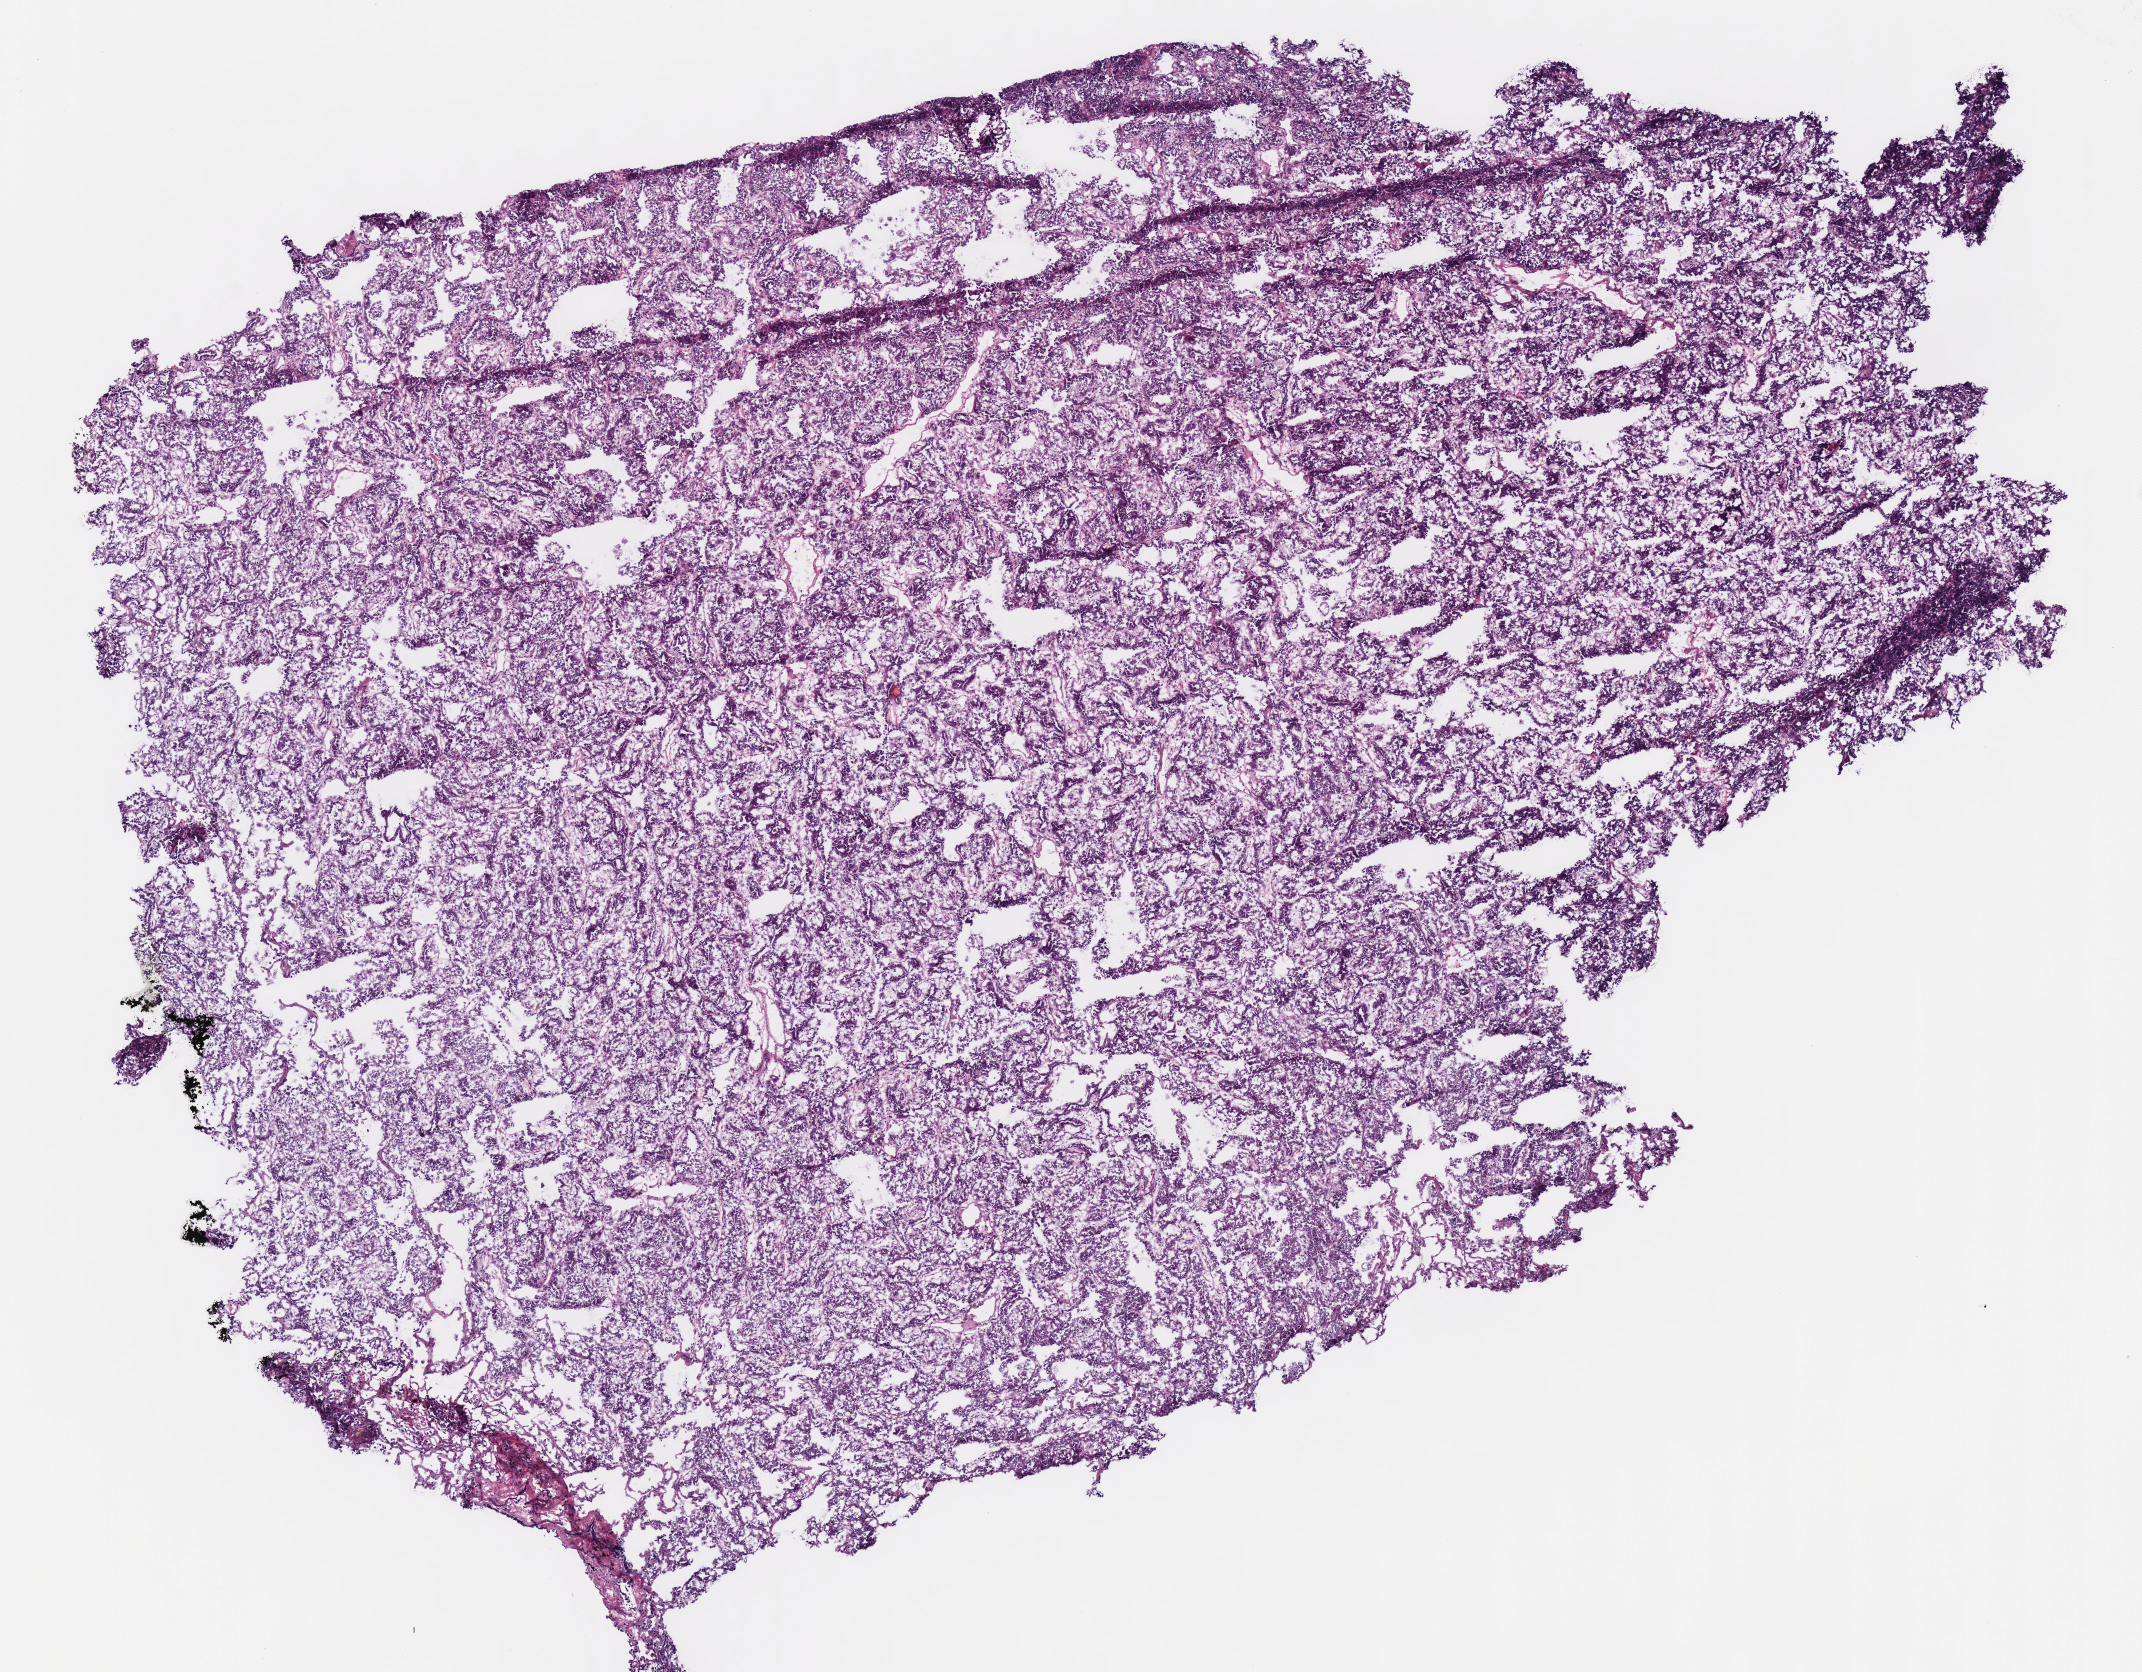
Whole-slide histology image, Hematoxylin and eosin (H&E) stained, whole scanned area (about 8.4 x 6.6 mm, acquisition: 40x scan) shown as a low-resolution overview; frozen section from the bottom of the tissue portion; lung, primary tumour sample. Patient: male, age at initial diagnosis 67 years. Pathologist review of this section (percent, as recorded): tumour cells 87%, tumour nuclei 80%, normal cells 3%, stromal cells 10%, necrosis 0%.
Pathologic diagnosis: Adenocarcinoma with mixed subtypes (upper lobe, lung). TNM: T2 N0 M0. AJCC pathologic stage: IB. Laterality: left.